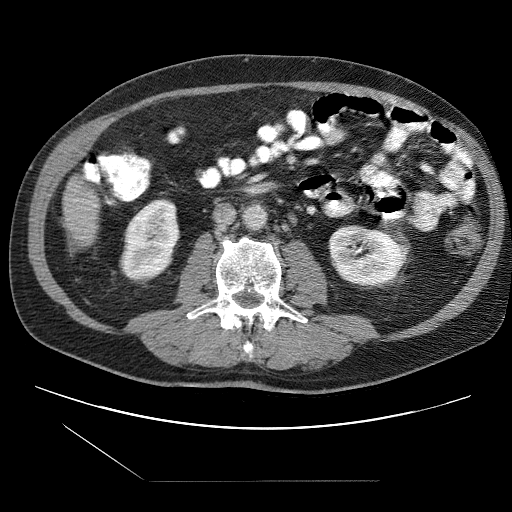
Contrast-enhanced abdominal CT (liver protocol), one axial slice; slice 11 of 109 in the series (ordered by position); reconstruction kernel STANDARD; one of 2 acquisitions stored at this slice position; soft-tissue window (W 400 / L 40 HU); 2.5 mm slice thickness; 512 × 512 image matrix, field of view 400 × 400 mm. Case-level facts recorded for this patient, not image findings: diagnosis: hepatocellular carcinoma (patient treated with transarterial chemoembolisation; whether this scan precedes or follows treatment is not stated here); TNM stage (as recorded): Stage-IIIB; Child-Pugh class: A; tumour differentiation: well differentiated; tumour nodularity: multinodular.
Annotated regions visible in this slice (semi-automatically segmented with operator editing):
- liver parenchyma outside the tumour (the mass and vessels are separate outlines, so this box may not span the whole liver): bounding box (x1, y1, x2, y2) in pixels: (64, 176, 100, 246)
- liver vessels: (90, 176, 98, 182)